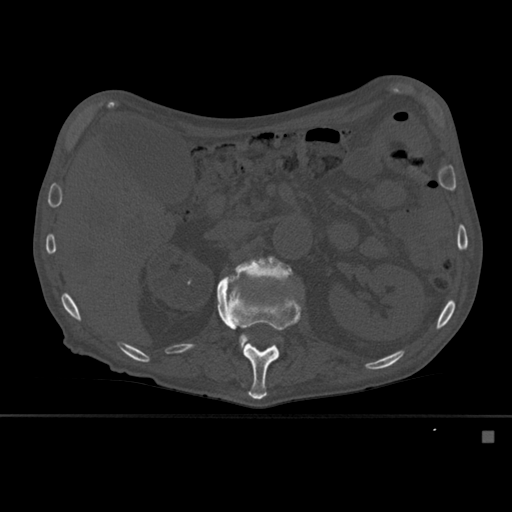
CT including the spine, one axial slice. Slice 250 of 527 in the series (ordered by position). Bone window (W 1800 / L 400 HU). 1.5 mm slice thickness. 512 × 512 image matrix. Patient: male, 78 years. Case-level facts recorded for this patient, not image findings: primary cancer: prostate.
Structures marked on this image (semi-automatically segmented with operator editing):
- L1 vertebra: box from (x=216, y=278) to (x=301, y=400) px
- L2 vertebra: (x=235, y=256)–(x=292, y=347)